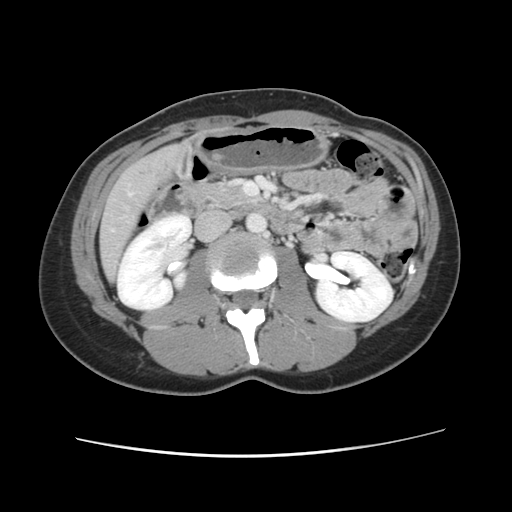
Contrast-enhanced abdominal CT, one axial slice. Position 31 of 134 along the scan axis. Intravenous contrast given. Soft-tissue window (W 400 / L 40 HU). 2.5 mm slice thickness. 512 × 512 image matrix, field of view 339 × 339 mm. Female patient, age 33 years. From the clinical record (not read from this slice): diagnosis: colorectal cancer liver metastases, imaged before liver resection; multiple liver metastases: yes; largest metastasis: 4.5 cm; chemotherapy before resection: no.
Outlined on this slice (manually delineated by an expert):
- liver: bounding box <100,144,191,282> (left, top, right, bottom; pixels)
- planned liver remnant (the part of the liver to remain after resection): <100,243,119,282>
- liver metastasis: <136,158,171,180>